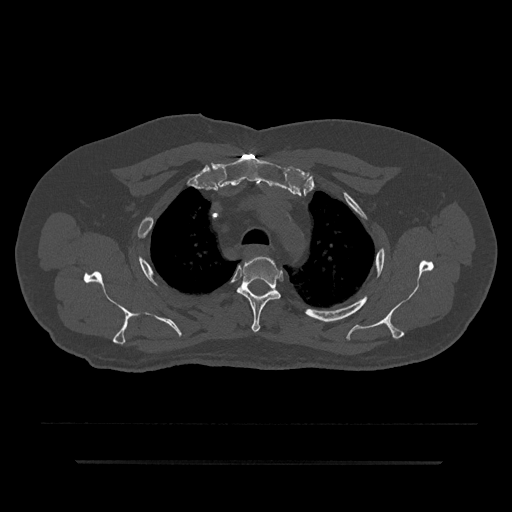
CT including the spine, one axial slice; position 655 of 797 along the scan axis; reconstruction kernel Br40s/3; bone window (W 1800 / L 400 HU); 0.5 mm slice thickness; 512 × 512 image matrix, field of view 464 × 464 mm. Male patient, age 59 years. From the clinical record (not read from this slice): primary cancer: bile ducts; vertebrae with lytic lesions (as recorded): T10.
Outlined on this slice (semi-automatically segmented with operator editing):
- T3 vertebra: bounding box (x1, y1, x2, y2) in pixels: (236, 256, 281, 333)